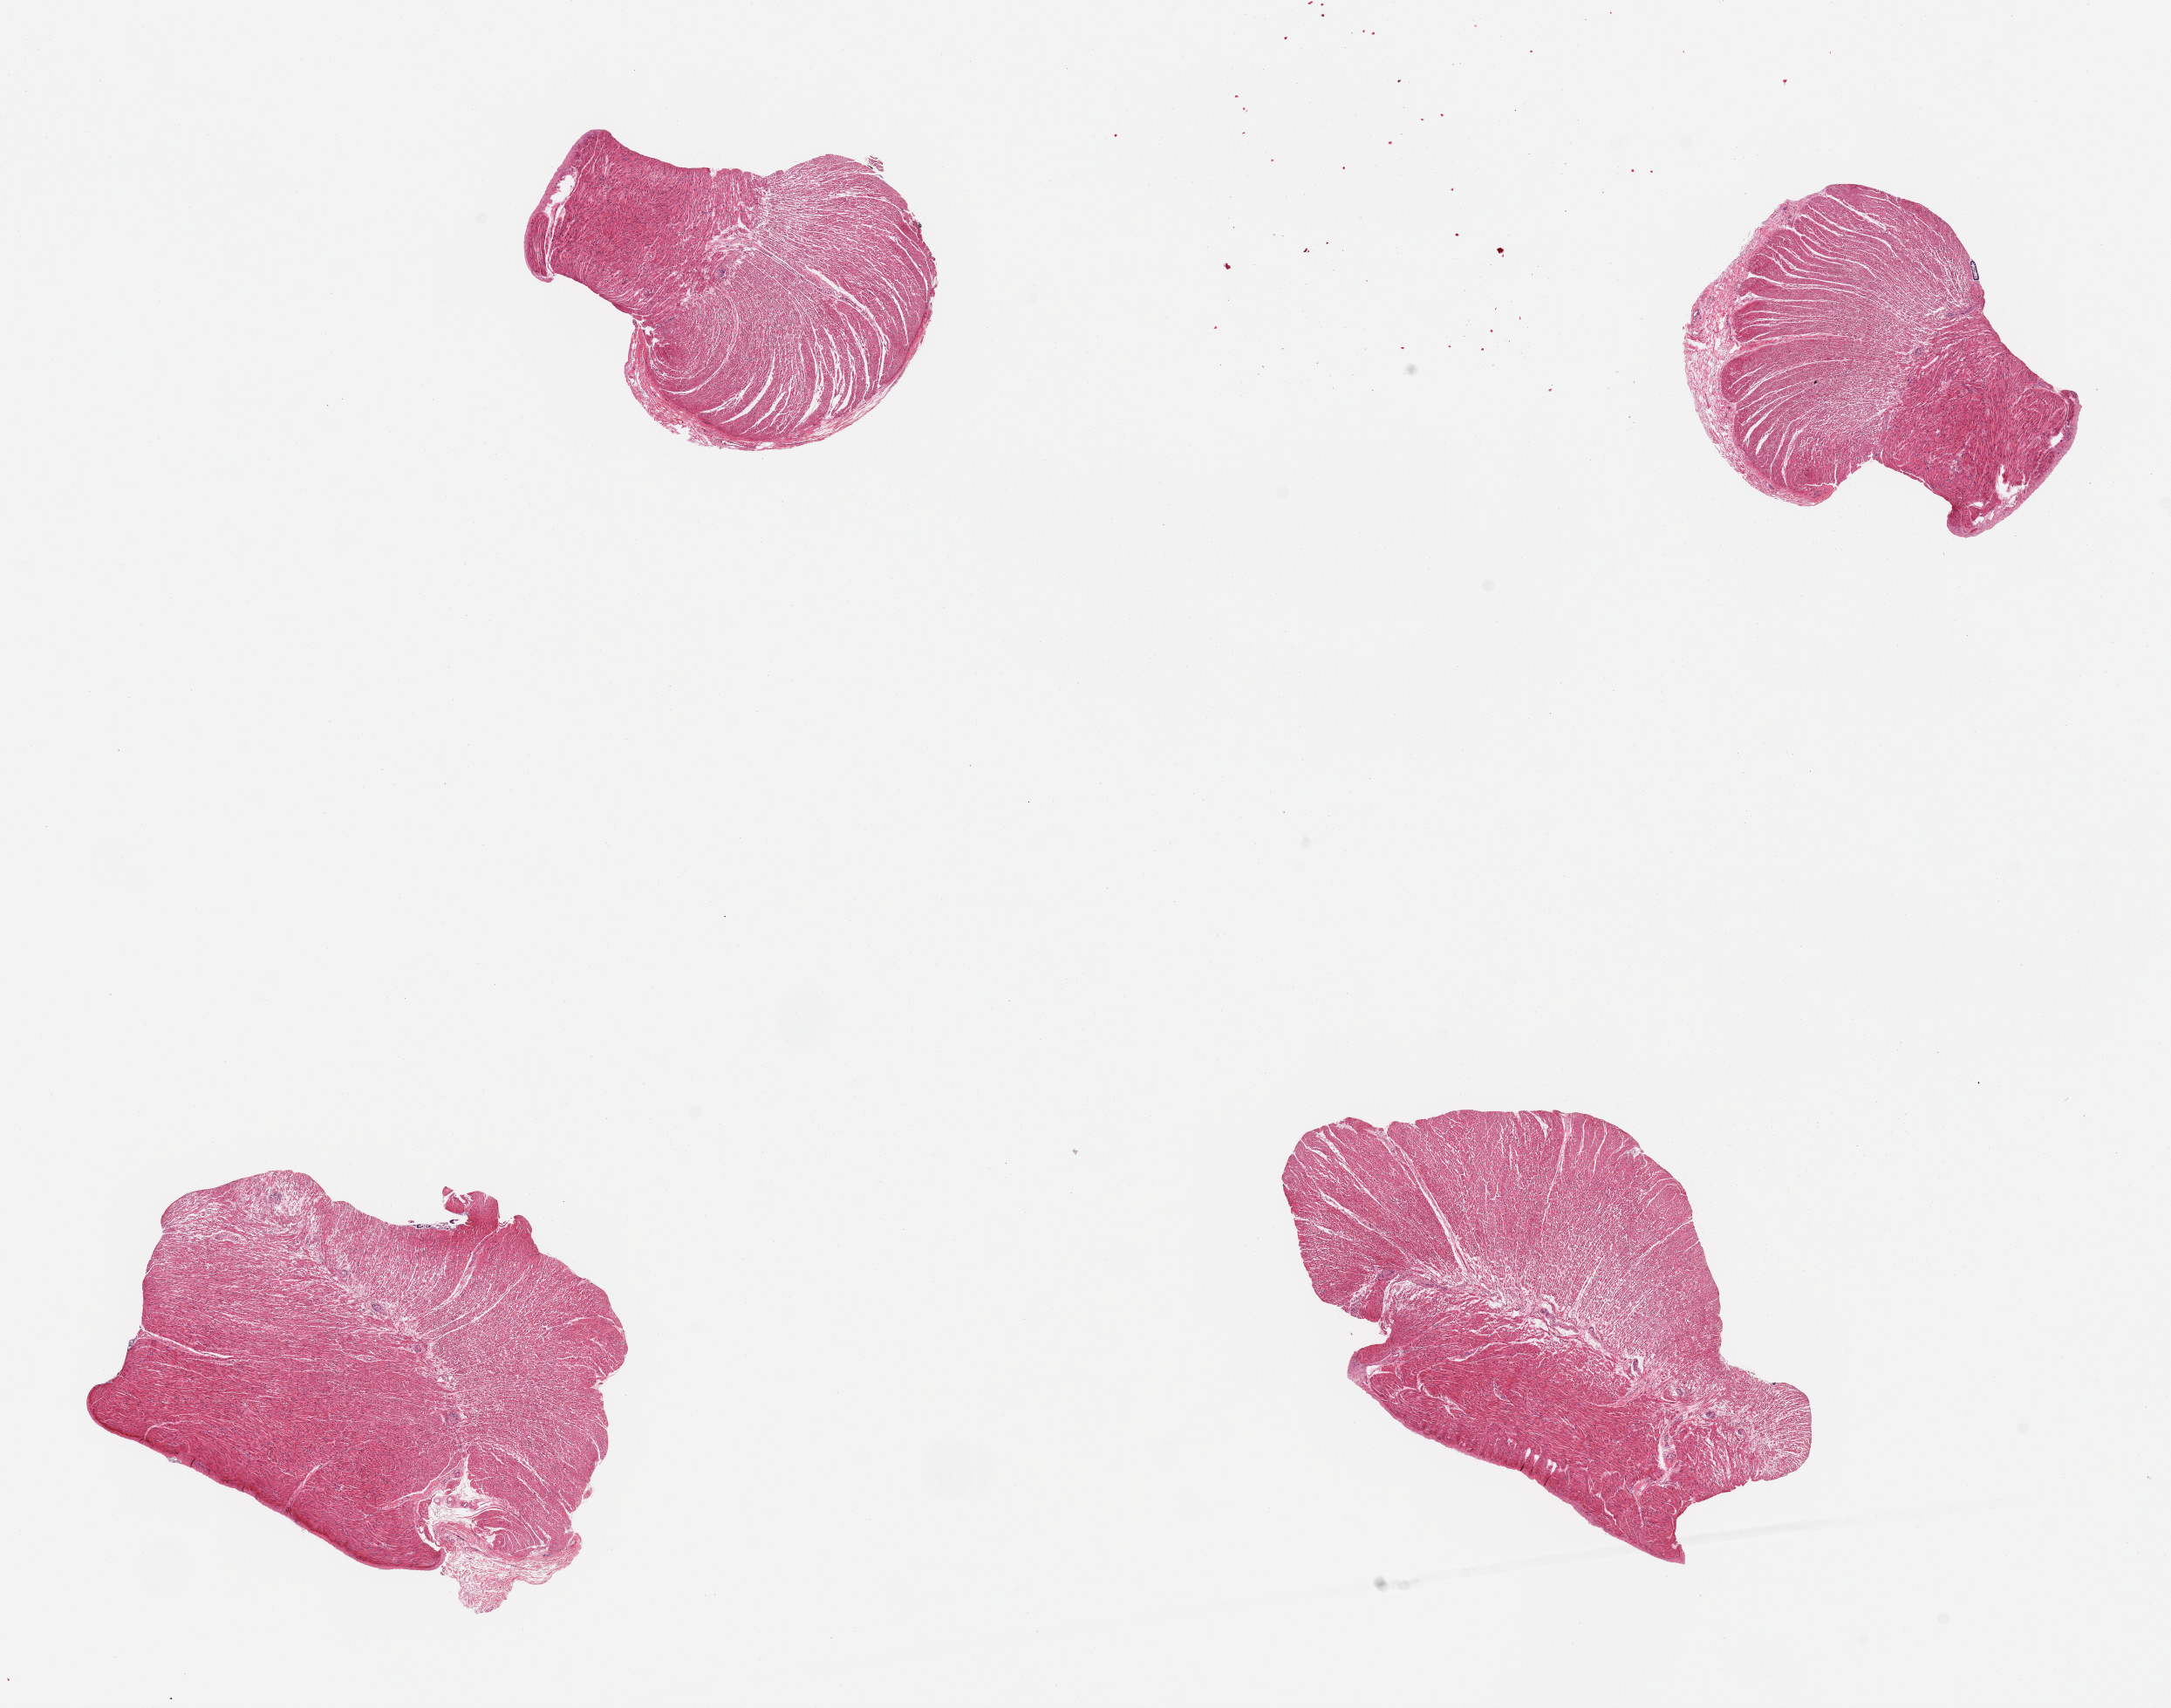
Haematoxylin and eosin whole-slide image, brightfield, a low-resolution overview of the entire scanned area, about 19.7 x 15.5 mm (from a 20x scan). PAXgene-fixed, paraffin-embedded tissue. Sampled site (target tissue): sigmoid colon. Donor tissue sample.
* pathologist's review note for this sample: 4 pieces; well dissected muscle